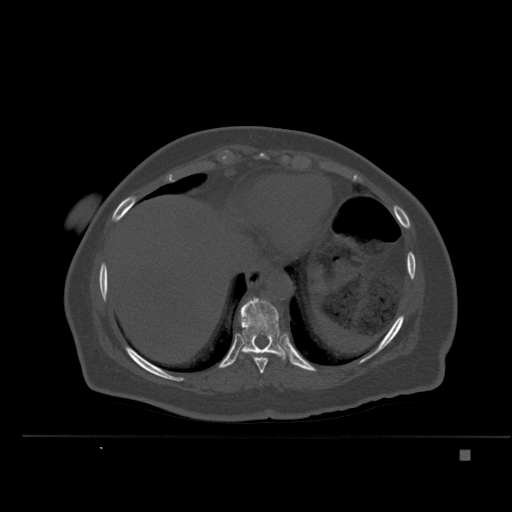
CT including the spine, one axial slice. Position 288 of 477 along the scan axis. Bone window (W 1800 / L 400 HU). 1.5 mm slice thickness. 512 × 512 image matrix, field of view 422 × 422 mm. Female patient, age 74 years. From the clinical record (not read from this slice): primary cancer: colon.
Structures marked on this image (semi-automatically segmented with operator editing):
- T10 vertebra: bounding box <240,297,286,360> (left, top, right, bottom; pixels)
- T9 vertebra: <244,352,273,374>